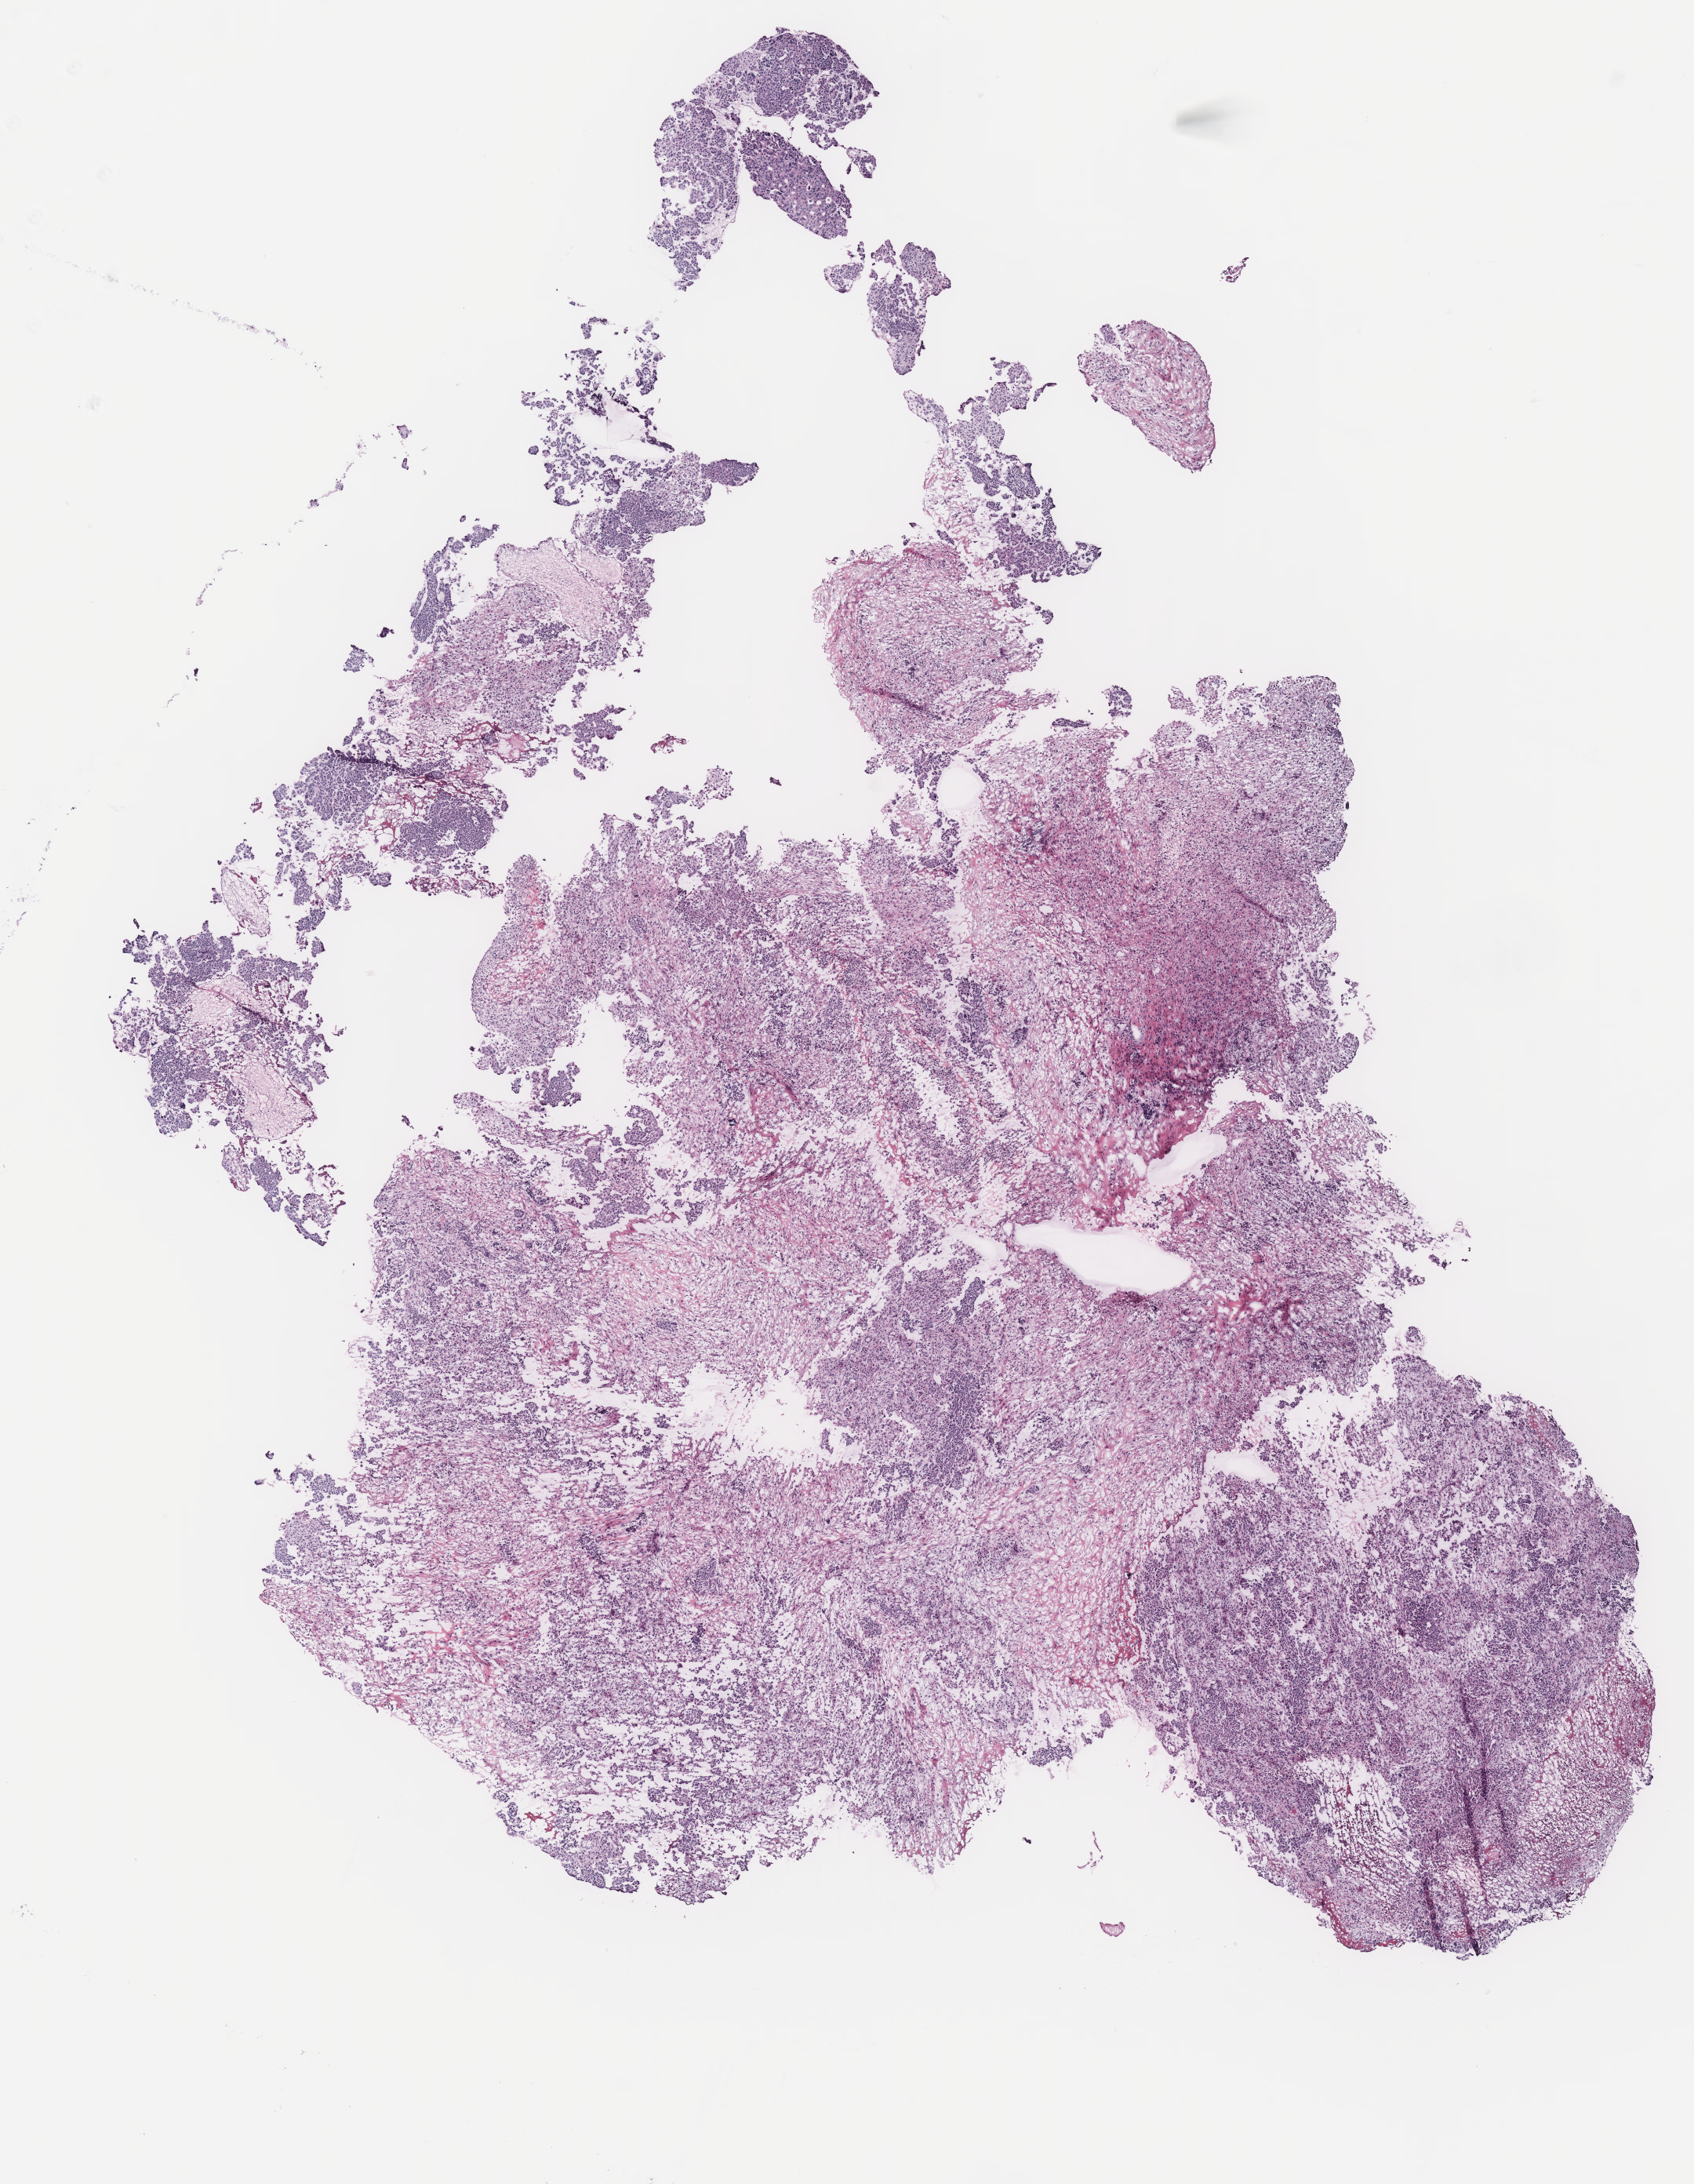
Whole-slide histology image, H&E-stained, low-resolution overview of the scanned area, about 8.6 x 11.1 mm (acquisition: 40x scan). Tumour tissue sample, ovary. 51-year-old female patient.
* histologic diagnosis: Serous adenocarcinoma, NOS (peritoneum, NOS)
* primary tumour site (as recorded): peritoneum